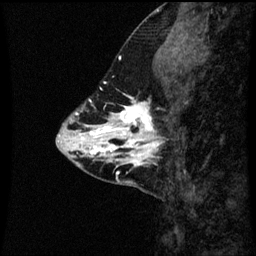
Breast MRI (dynamic contrast-enhanced), one sagittal slice. Position 20 of 60 along the scan axis. Dynamic contrast-enhanced series, image 2 of 3 at this slice position (ordered by acquisition). 1.5 T. TE 4.2 ms, TR 8.9 ms. 2 mm slice thickness. 256 × 256 image matrix, field of view 200 × 200 mm. Patient: female, 43 years. From the clinical record (not read from this slice): setting: breast cancer imaged before/during neoadjuvant chemotherapy; receptor status: HR-positive, HER2-negative.
Structures marked on this image (semi-automatic segmentation, software-assisted and operator-edited):
- analysis volume of interest (the breast-tissue region the enhancement analysis was run in; not a lesion): bounding box <110,100,164,163> (left, top, right, bottom; pixels)
- tumour enhancement mask (voxels above the 70 % enhancement threshold inside the analysis volume of interest): <110,100,159,163>